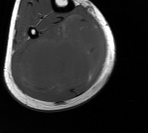
MRI of an extremity soft-tissue mass, one axial slice. Slice 63 of 76 in the series (ordered by position). MR volume resampled by the dataset authors to the PET/CT grid (not the native acquisition matrix). 3.27 mm slice thickness. 148 × 133 image matrix, field of view 145 × 130 mm. Male patient. From the clinical record (not read from this slice): histological type: liposarcoma - round cell; grade: high; site of the primary tumour: right calf.
Outlined on this slice (expert contour drawn on MRI and transferred to this co-registered scan by the dataset authors):
- gross tumour volume (mass): bounding box <15,17,103,95> (left, top, right, bottom; pixels)